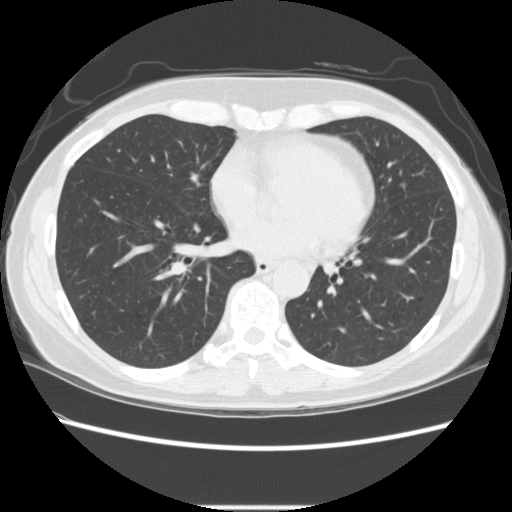
Chest CT (low-dose screening protocol), one axial image; baseline annual screen; lung window (W 1500 / L -600 HU); slice 146 of 256 in the series; 512 × 512 image matrix. Female, age 60 years at enrolment.
• Expert-annotated lung lesion, bounding box (x1, y1, x2, y2) in pixels: (391, 176, 419, 202).
• No non-calcified nodule or mass ≥4 mm was recorded by the screening reader at this exam.
• Lung cancer was diagnosed 939 days after this screen: adenocarcinoma, NOS, lingula, poorly differentiated (G3), stage IA (AJCC 6th edition), 6 mm at pathology.